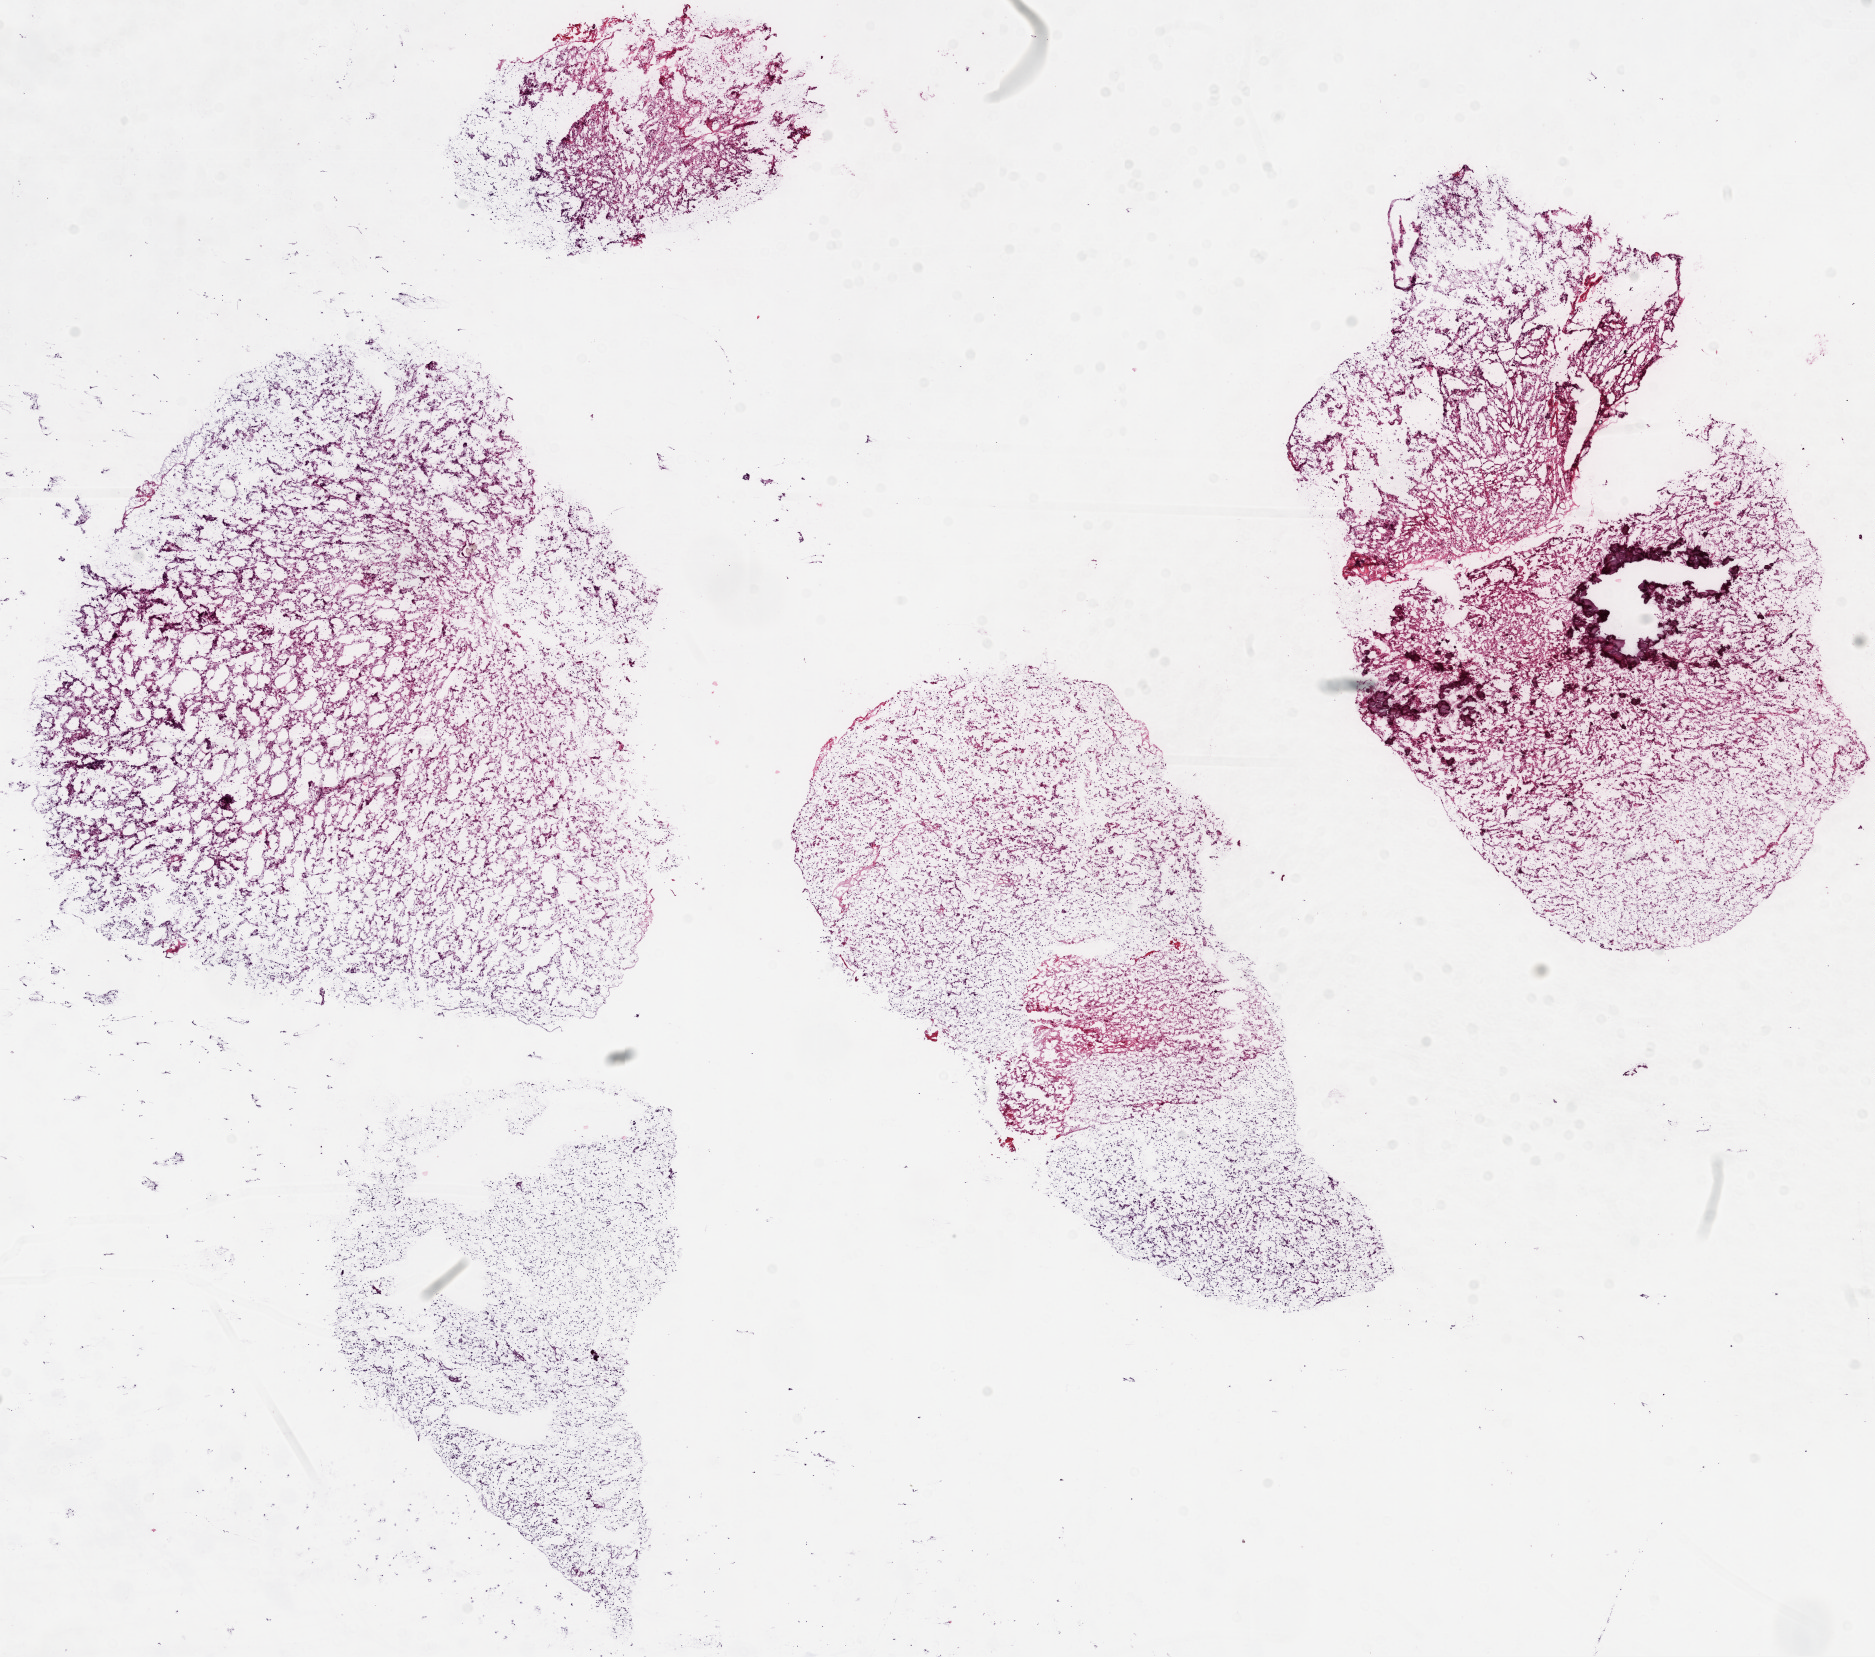
Digitized H&E tissue section (whole slide), whole scanned area (about 15.0 x 13.3 mm, slide scanned at 20x) shown as a low-resolution overview; frozen section from the top of the tissue portion; brain, primary tumour sample. Male patient; age at initial diagnosis 54 years. Pathologist review of this section (percent, as recorded): tumour cells 95%, tumour nuclei 100%, normal cells 0%, stromal cells 0%, necrosis 5%.
- histologic diagnosis: Glioblastoma